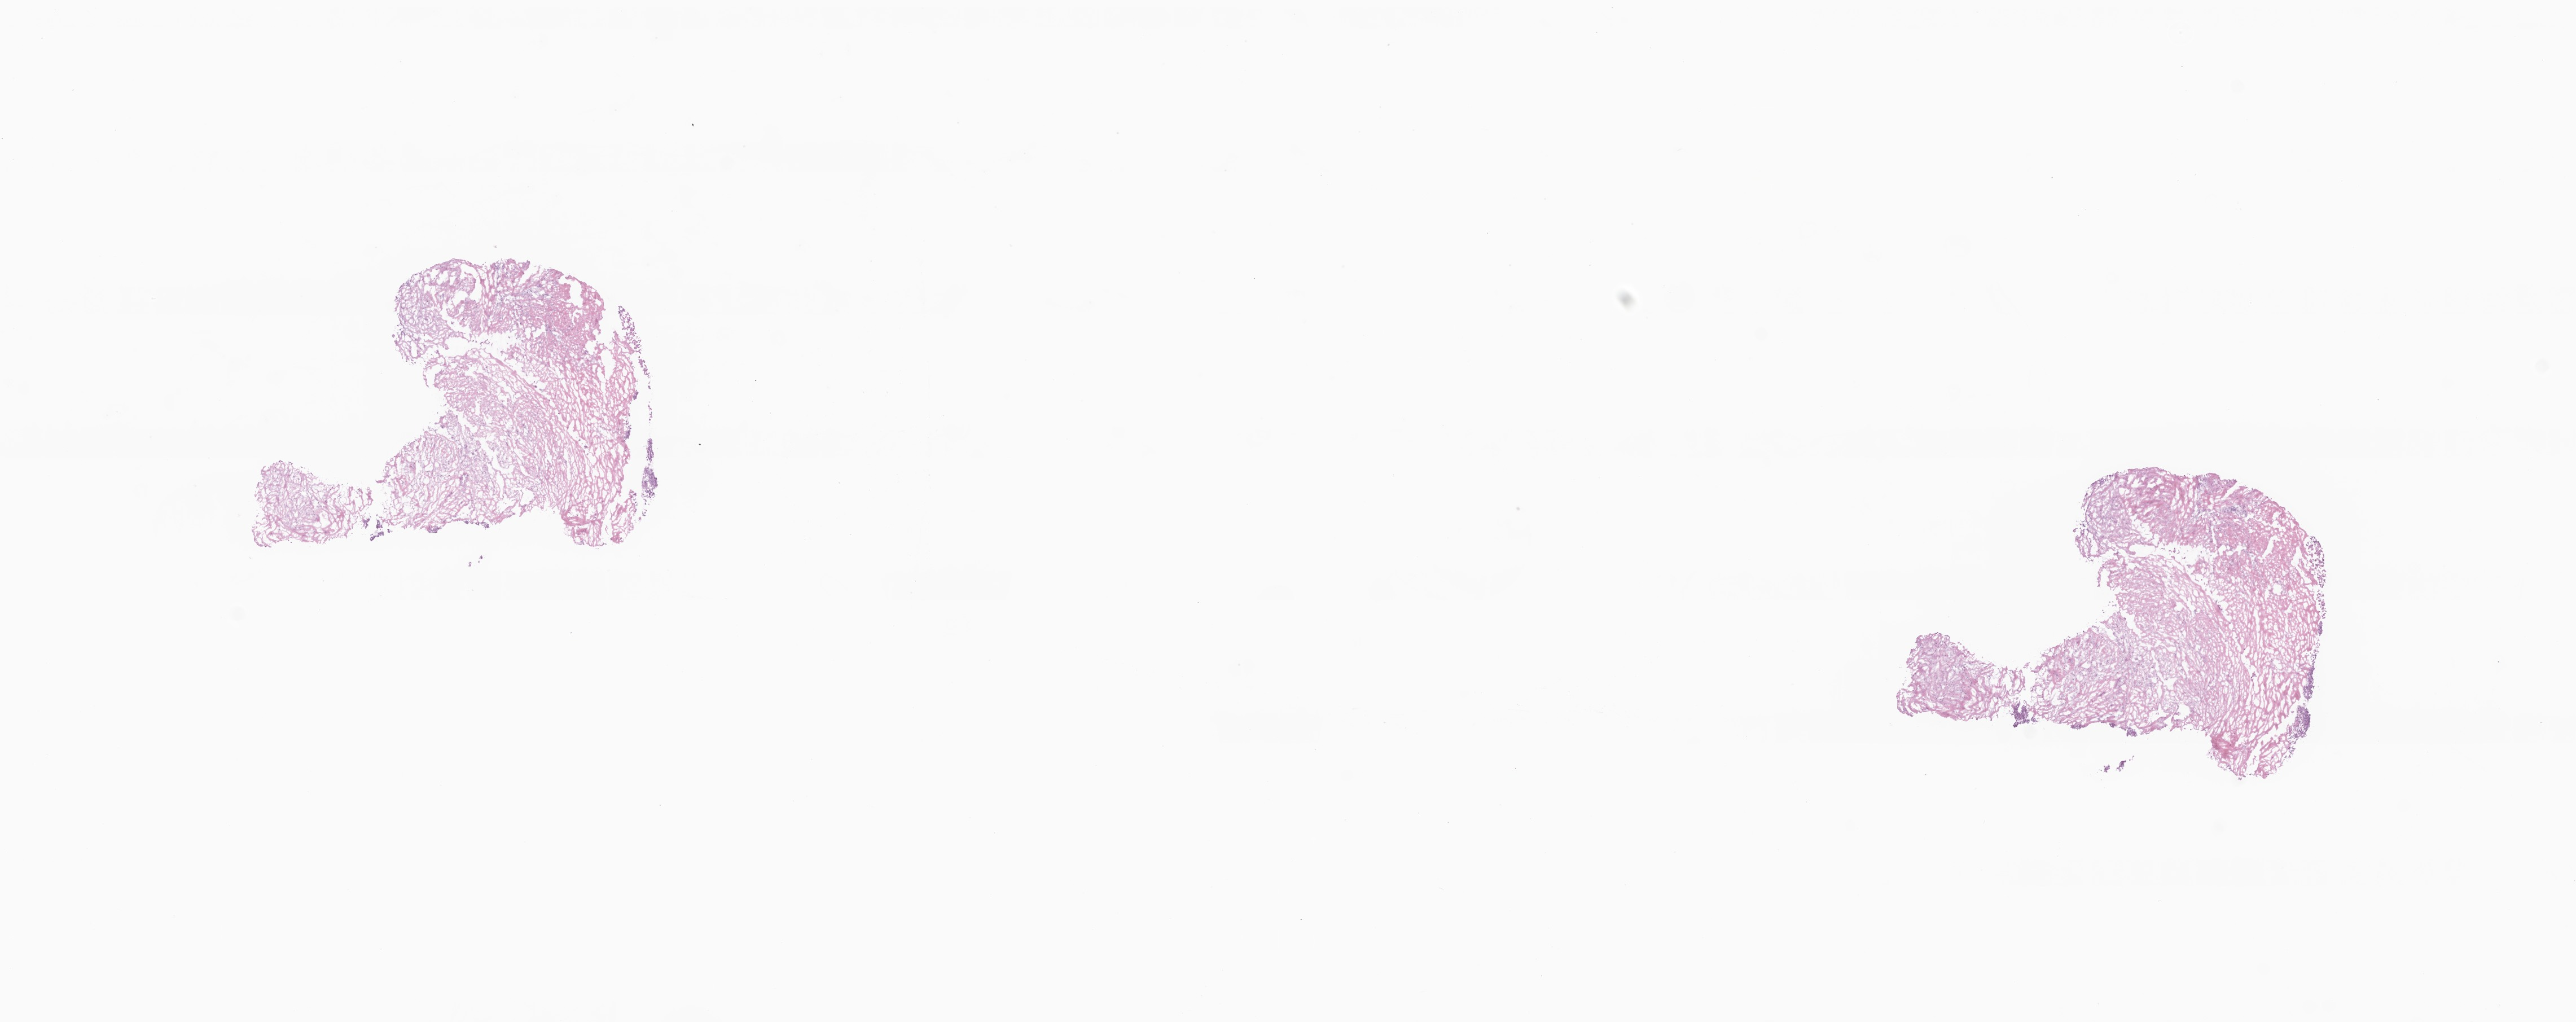
H&E whole-slide image — a low-resolution overview of the entire scanned area, about 19.2 x 7.6 mm. Frozen section (tissue freezing medium). Metastatic tumor tissue, resected from pelvis. Patient: male, age at initial diagnosis 61 years.
Patient diagnosis (primary): Adenocarcinoma, NOS.